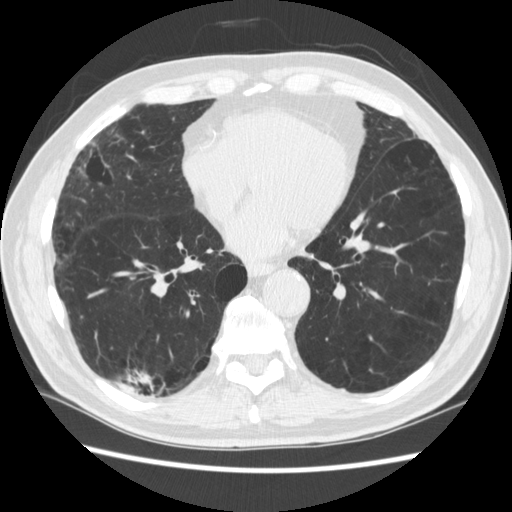
Low-dose screening chest CT, one axial slice. Reconstruction kernel STANDARD. Lung window (W 1500 / L -600 HU). 1.25 mm slice thickness. 512 × 512 image matrix, field of view 360 × 360 mm.
Outlined on this slice (outlined manually by an expert reader):
- lesion 1 (tumor, upper lobe of right lung): bounding box [x1, y1, x2, y2] px = [140, 376, 150, 384]